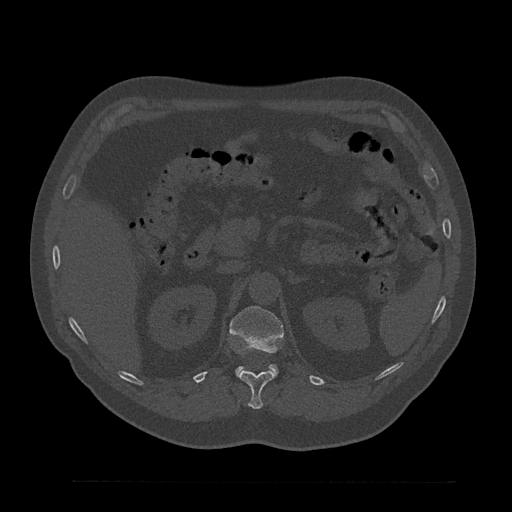
CT including the spine, one axial slice. Slice 201 of 797 in the series (ordered by position). Bone window (W 1800 / L 400 HU). 0.5 mm slice thickness. 512 × 512 image matrix, field of view 430 × 430 mm. Patient: male, 61 years. Case-level facts recorded for this patient, not image findings: primary cancer: prostate.
Annotated regions visible in this slice (semi-automatically segmented with operator editing):
- L1 vertebra: bounding box (x1, y1, x2, y2) in pixels: (230, 306, 284, 376)
- T12 vertebra: (239, 371, 275, 409)